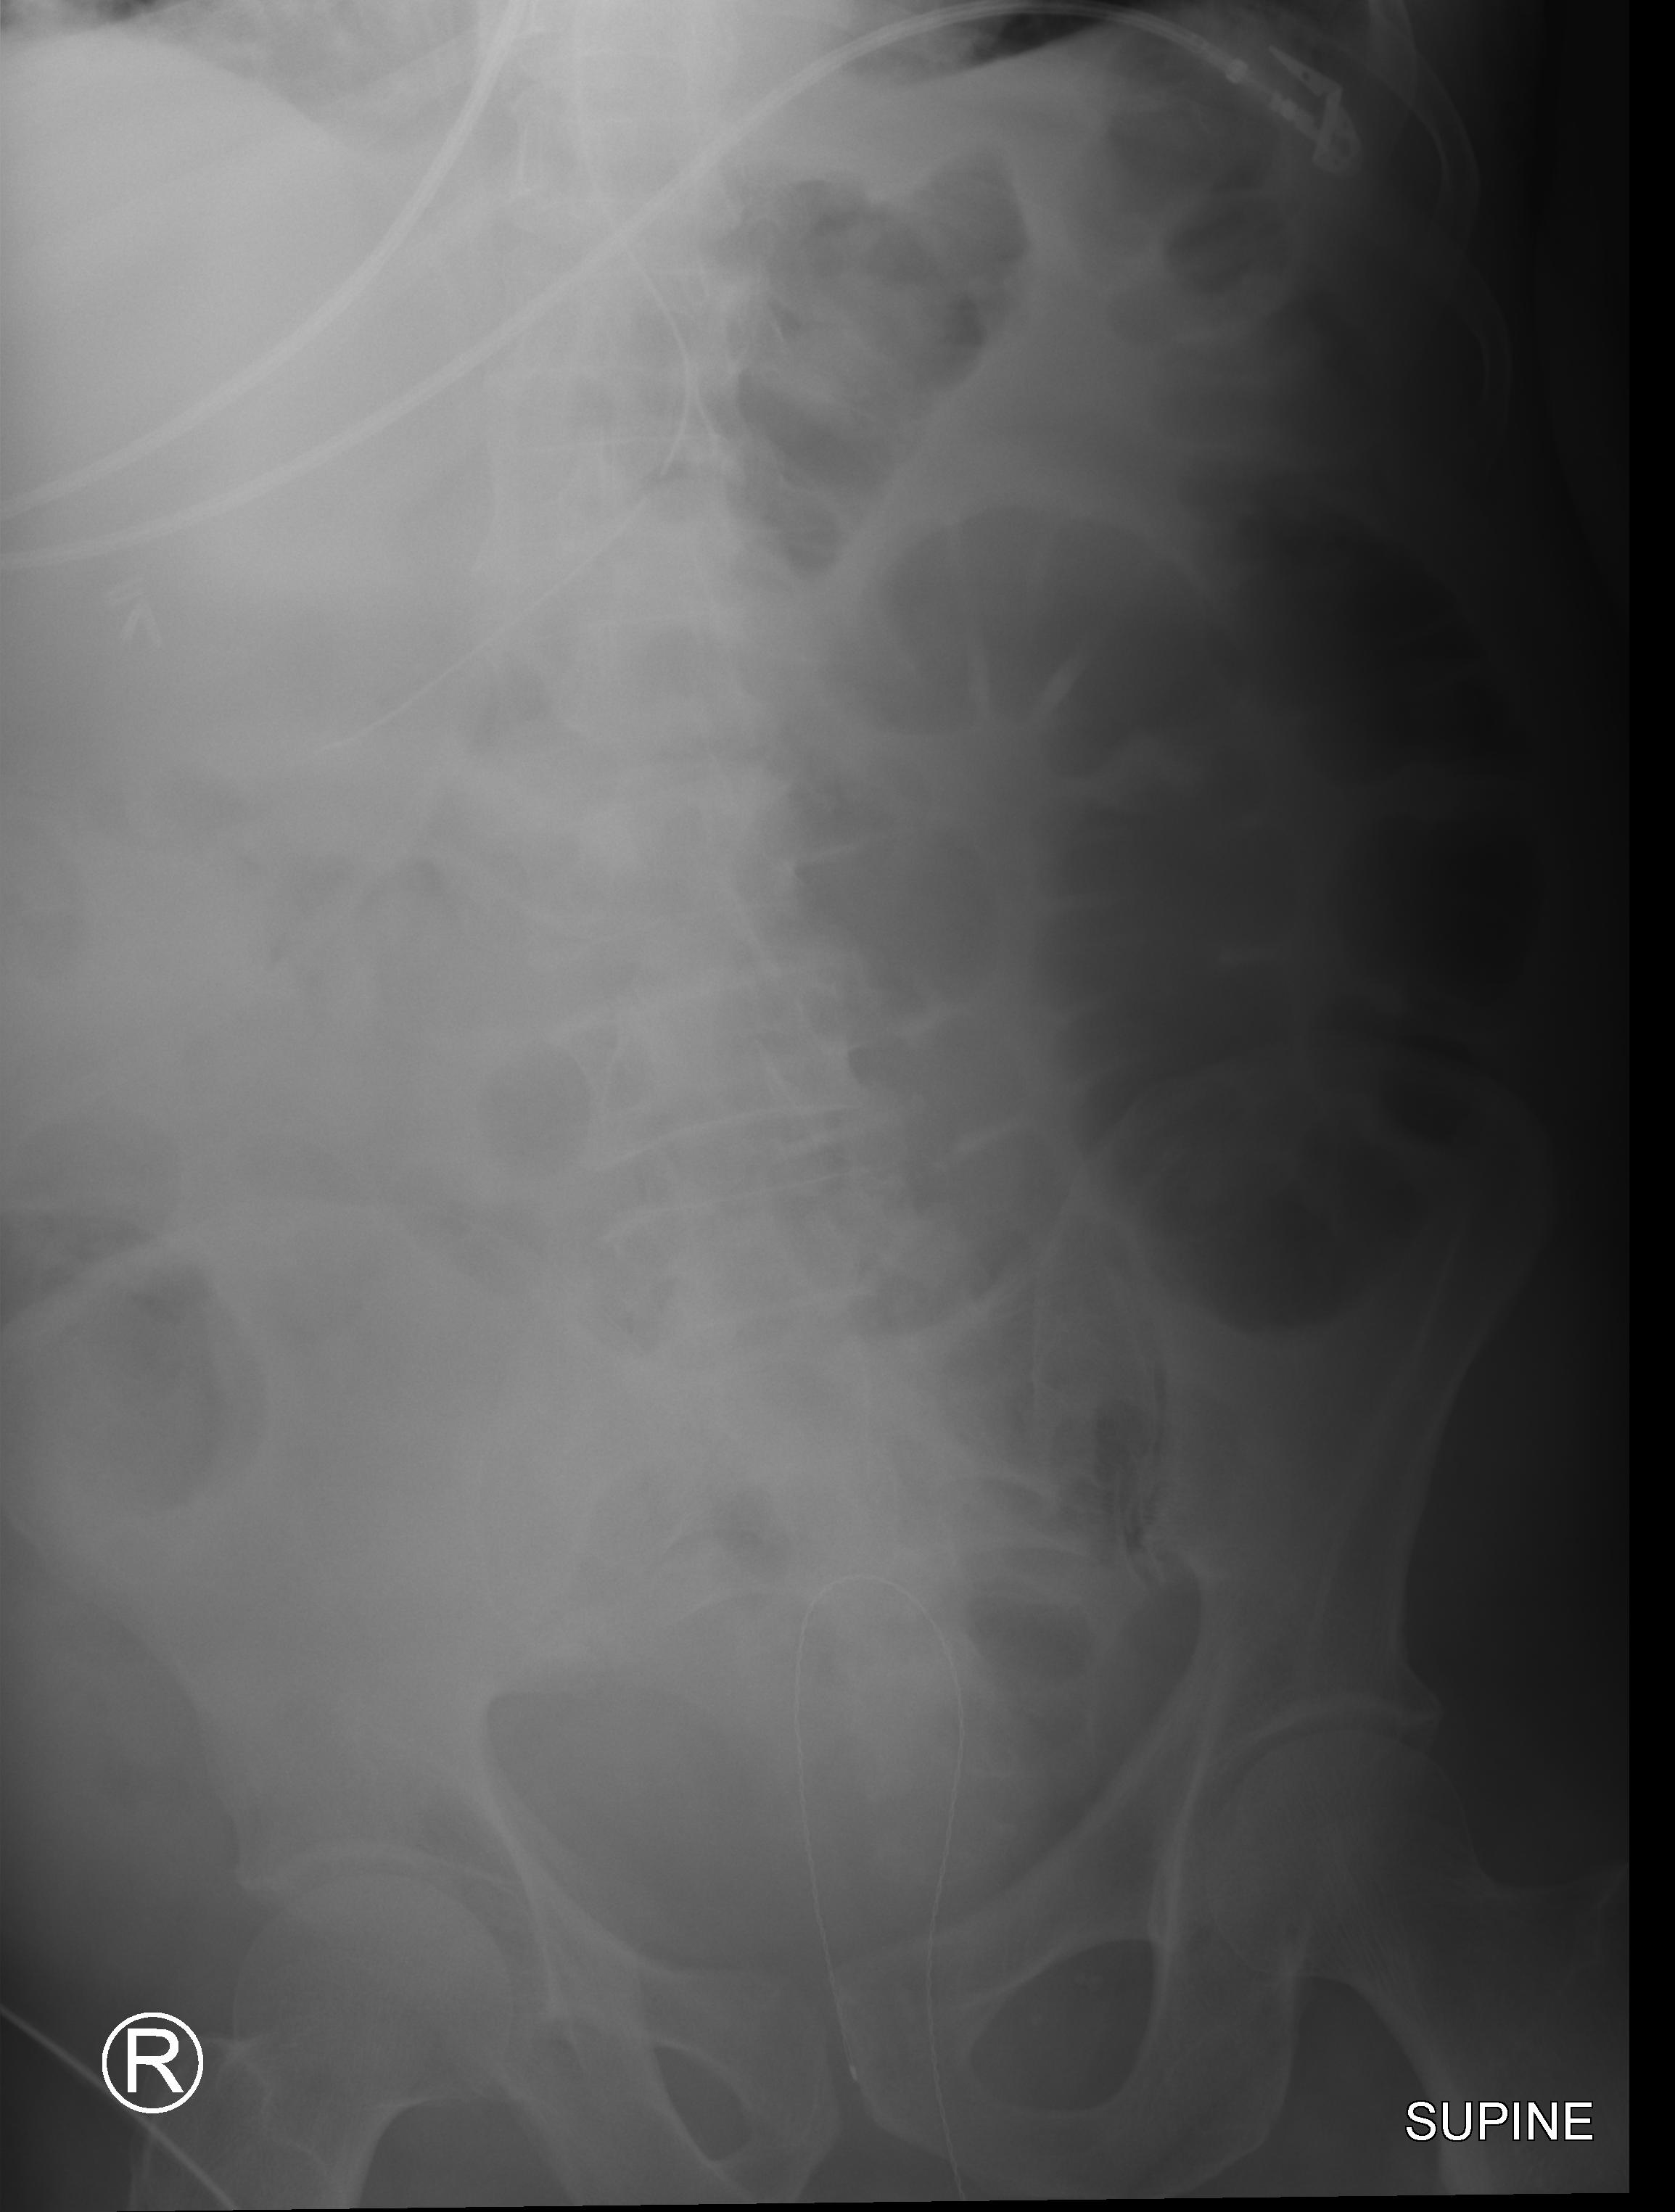
Portable abdomen radiograph, anteroposterior (AP) projection. Patient hospitalised with COVID-19; male, aged 75–90 years.
Hospital-stay facts (about this admission, not read from this image; timing relative to this image not recorded):
- mechanically ventilated during this hospital stay: yes
- admitted to intensive care during this hospital stay: yes
- other chronic lung disease (admission record): yes